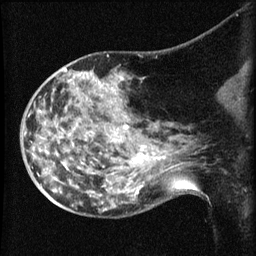
Breast MRI (dynamic contrast-enhanced), one sagittal slice. Slice 32 of 60 in the series (ordered by position). Dynamic contrast-enhanced series, image 2 of 3 at this slice position (ordered by acquisition). 1.5 T. TE 4.2 ms, TR 8.2 ms. 2.1 mm slice thickness. 256 × 256 image matrix. Female patient, age 50 years.
Outlined on this slice (semi-automatic segmentation, software-assisted and operator-edited):
- analysis volume of interest (the breast-tissue region the enhancement analysis was run in; not a lesion): bounding box <38,74,169,211> (left, top, right, bottom; pixels)
- tumour enhancement mask (voxels above the 70 % enhancement threshold inside the analysis volume of interest): <123,125,145,162>